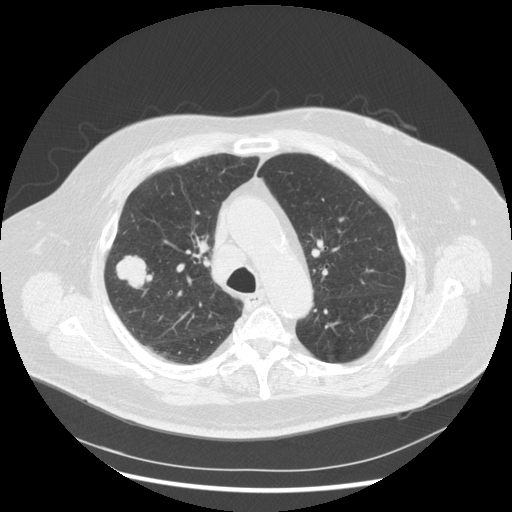
Low-dose screening chest CT, one axial slice. Position 195 of 263 along the scan axis. Reconstruction kernel STANDARD. 120 kVp. Lung window (W 1500 / L -600 HU). 2.5 mm slice thickness. 512 × 512 image matrix, field of view 400 × 400 mm.
Outlined on this slice (expert manual segmentation):
- lesion 1 (tumor, upper lobe of right lung): bounding box (x1, y1, x2, y2) in pixels: (116, 256, 152, 288)